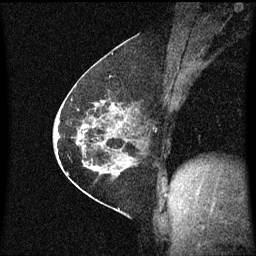
Breast MRI (dynamic contrast-enhanced), one sagittal slice. Slice 33 of 60 in the series (ordered by position). Dynamic contrast-enhanced series, image 2 of 3 at this slice position (ordered by acquisition). 1.5 T. TE 4.2 ms, TR 8.4 ms. 256 × 256 image matrix, field of view 200 × 200 mm. Female patient, age 60 years.
Structures marked on this image (semi-automatically segmented with operator editing):
- analysis volume of interest (the breast-tissue region the enhancement analysis was run in; not a lesion): bounding box <69,66,146,193> (left, top, right, bottom; pixels)
- tumour enhancement mask (voxels above the 70 % enhancement threshold inside the analysis volume of interest): <69,70,145,169>